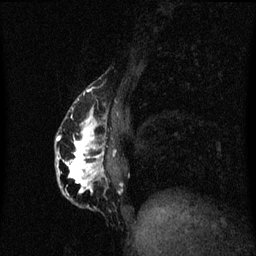
Breast MRI (dynamic contrast-enhanced), one sagittal slice; position 19 of 60 along the scan axis; dynamic contrast-enhanced series, image 2 of 3 at this slice position (ordered by acquisition); 1.5 T; TE 4.2 ms, TR 8.4 ms; 2 mm slice thickness; 256 × 256 image matrix, field of view 200 × 200 mm. Patient: female, 40 years.
Structures marked on this image (semi-automatically segmented with operator editing):
- analysis volume of interest (the breast-tissue region the enhancement analysis was run in; not a lesion): bounding box [x1, y1, x2, y2] px = [56, 84, 113, 209]
- tumour enhancement mask (voxels above the 70 % enhancement threshold inside the analysis volume of interest): [56, 108, 105, 193]